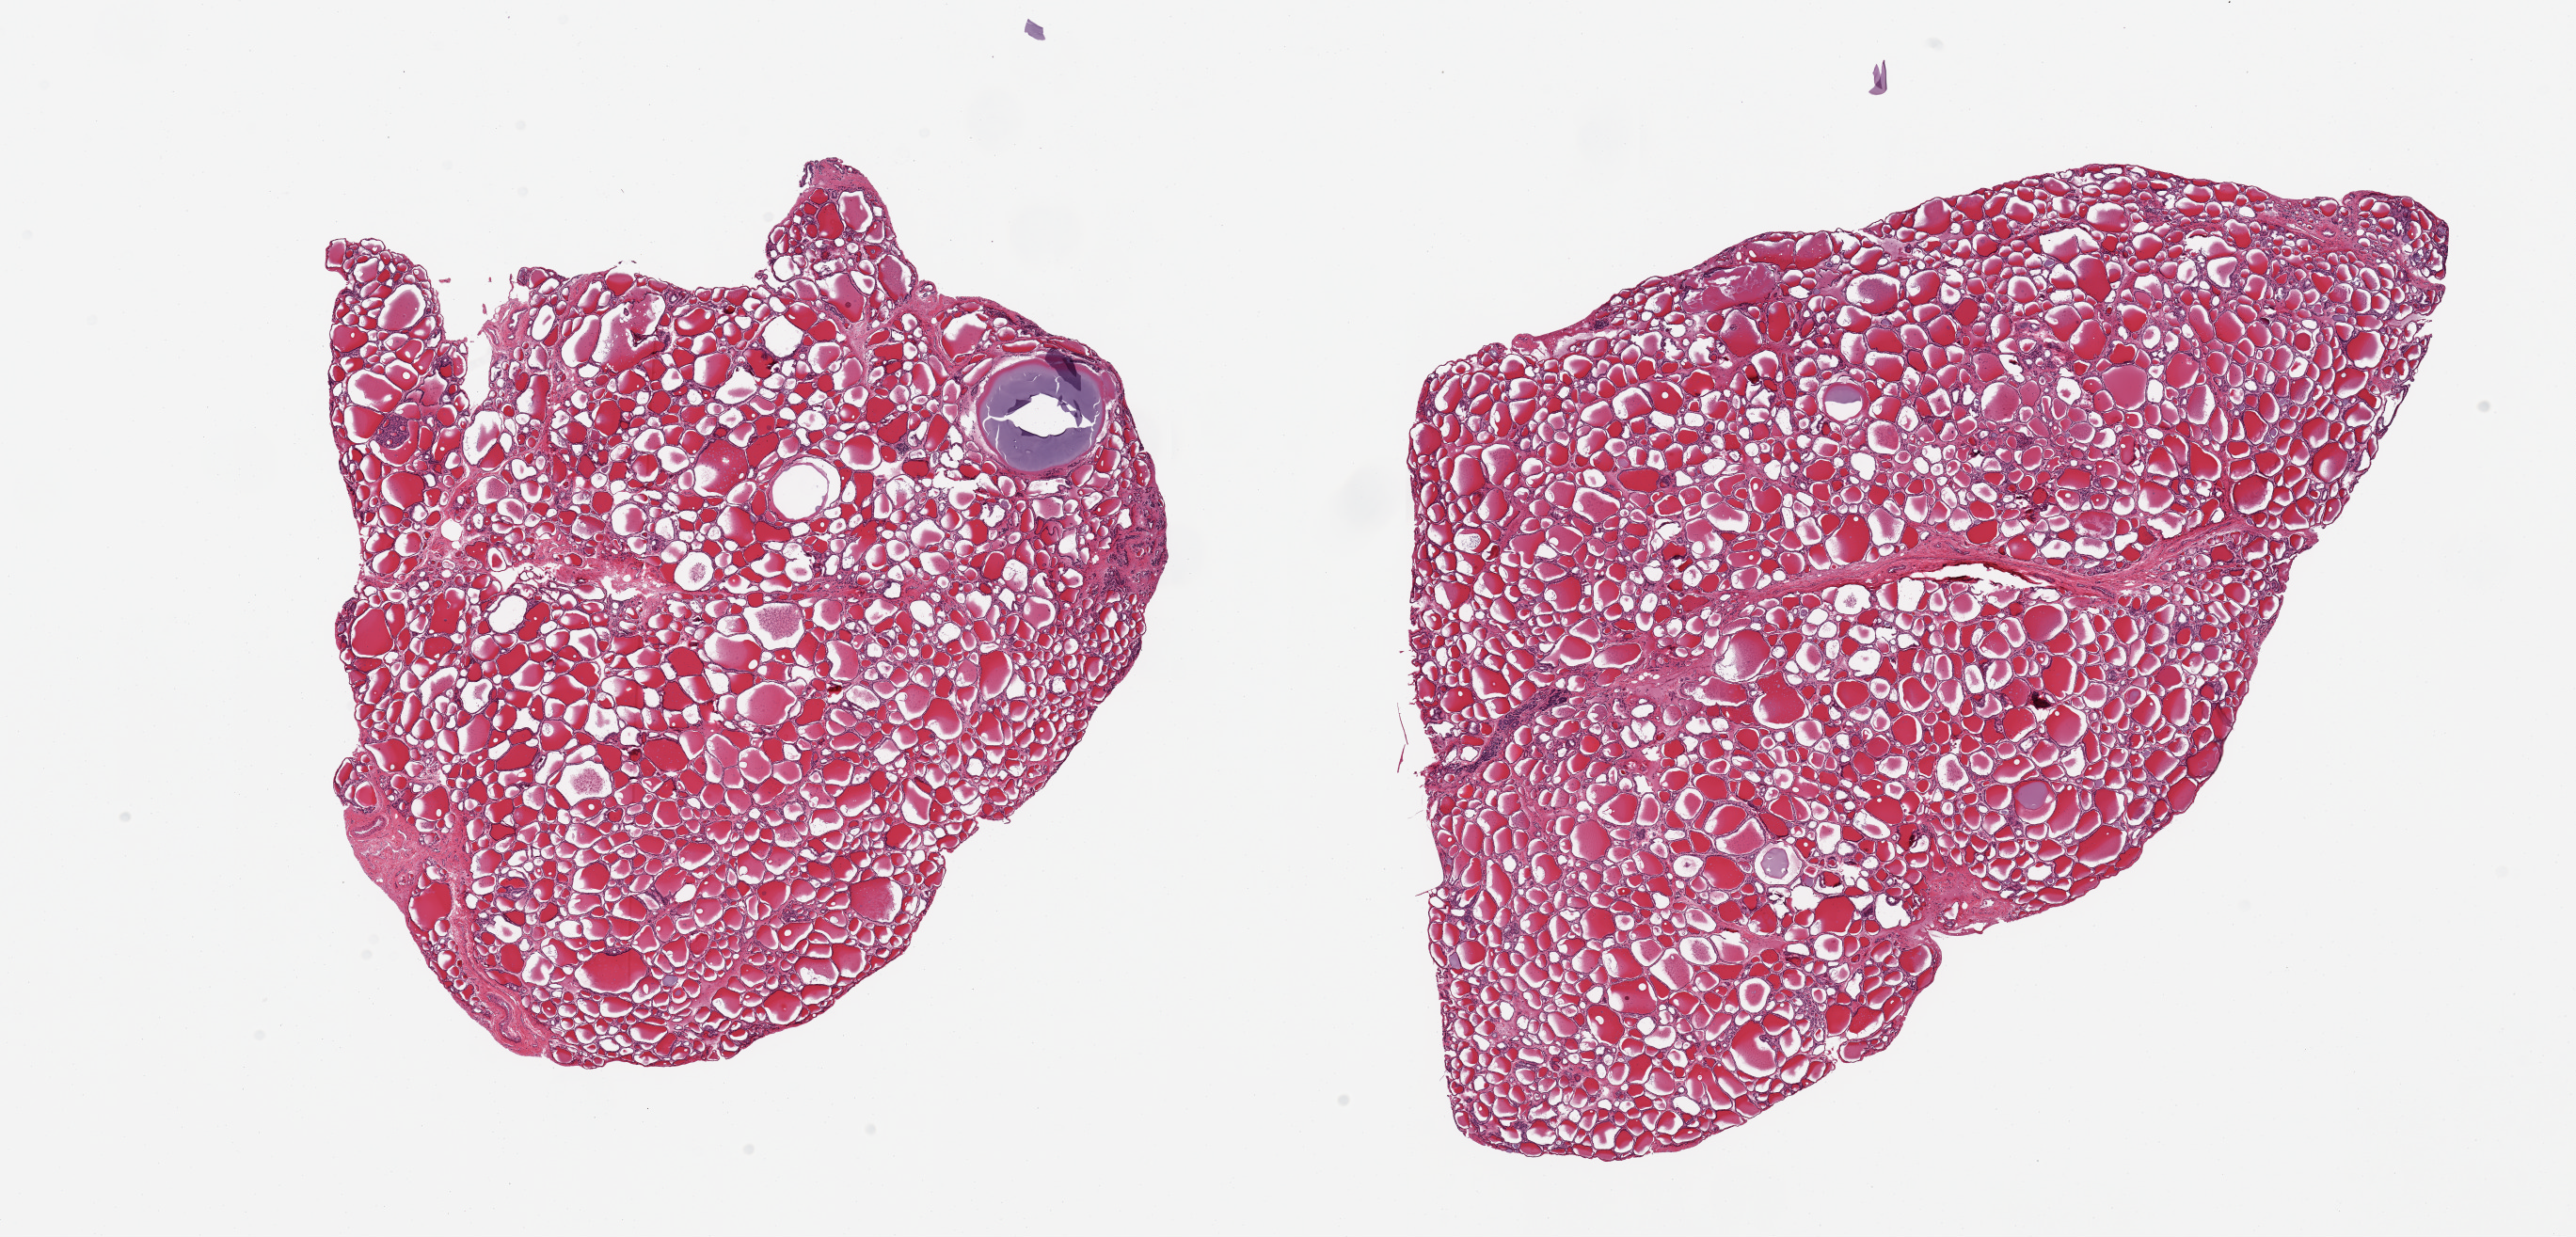
Whole-slide image, haematoxylin and eosin stain — whole scanned area (about 21.7 x 10.4 mm) shown as a low-resolution overview. PAXgene-fixed, paraffin-embedded tissue. Target tissue: thyroid. Tissue donor sample. Male donor.
Review note (as recorded): 2 pieces, no abnormalities.